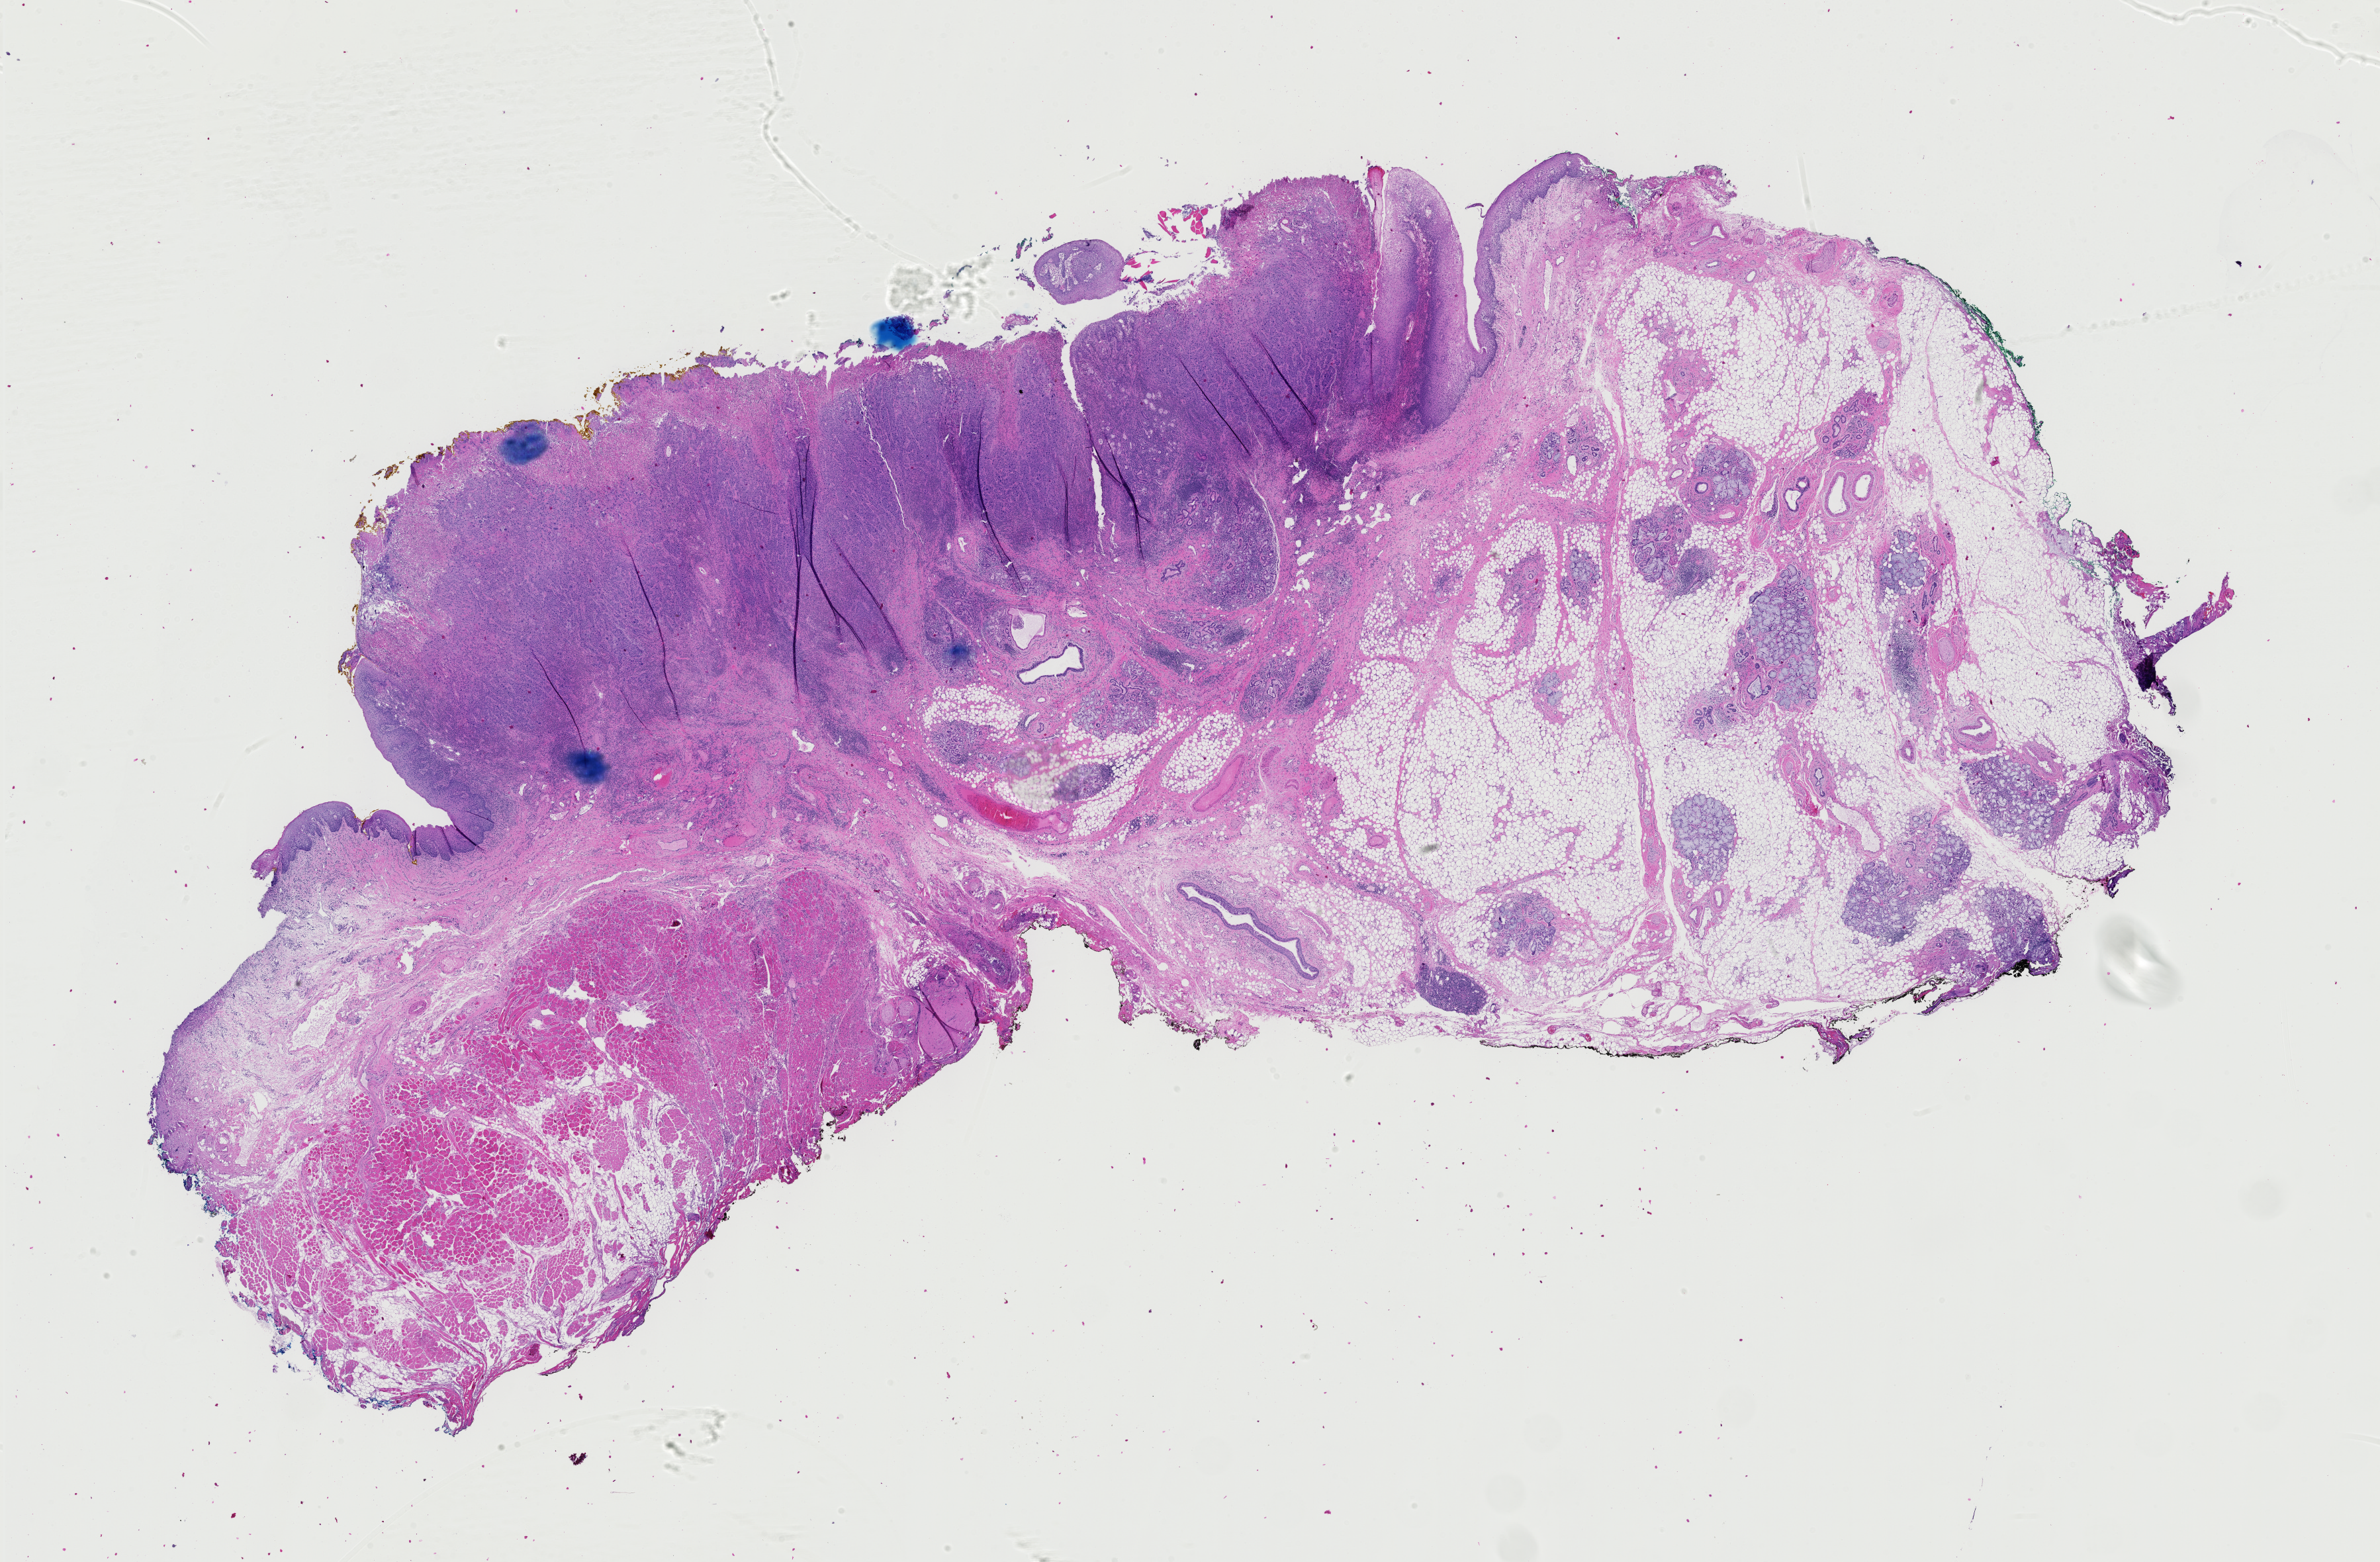
Digitized H&E tissue section (whole slide), a low-resolution overview of the entire scanned area, about 26.1 x 17.1 mm, FFPE section, sample: primary tumour, head and neck. Patient: male, age at initial diagnosis 71 years. Histologic grade: G3 (poorly differentiated).
AJCC pathologic stage: III (7th edition). Lymph nodes positive (case pathology): 1 of 40 examined. Diagnosis: Squamous cell carcinoma, NOS (floor of mouth, NOS). Laterality: left.